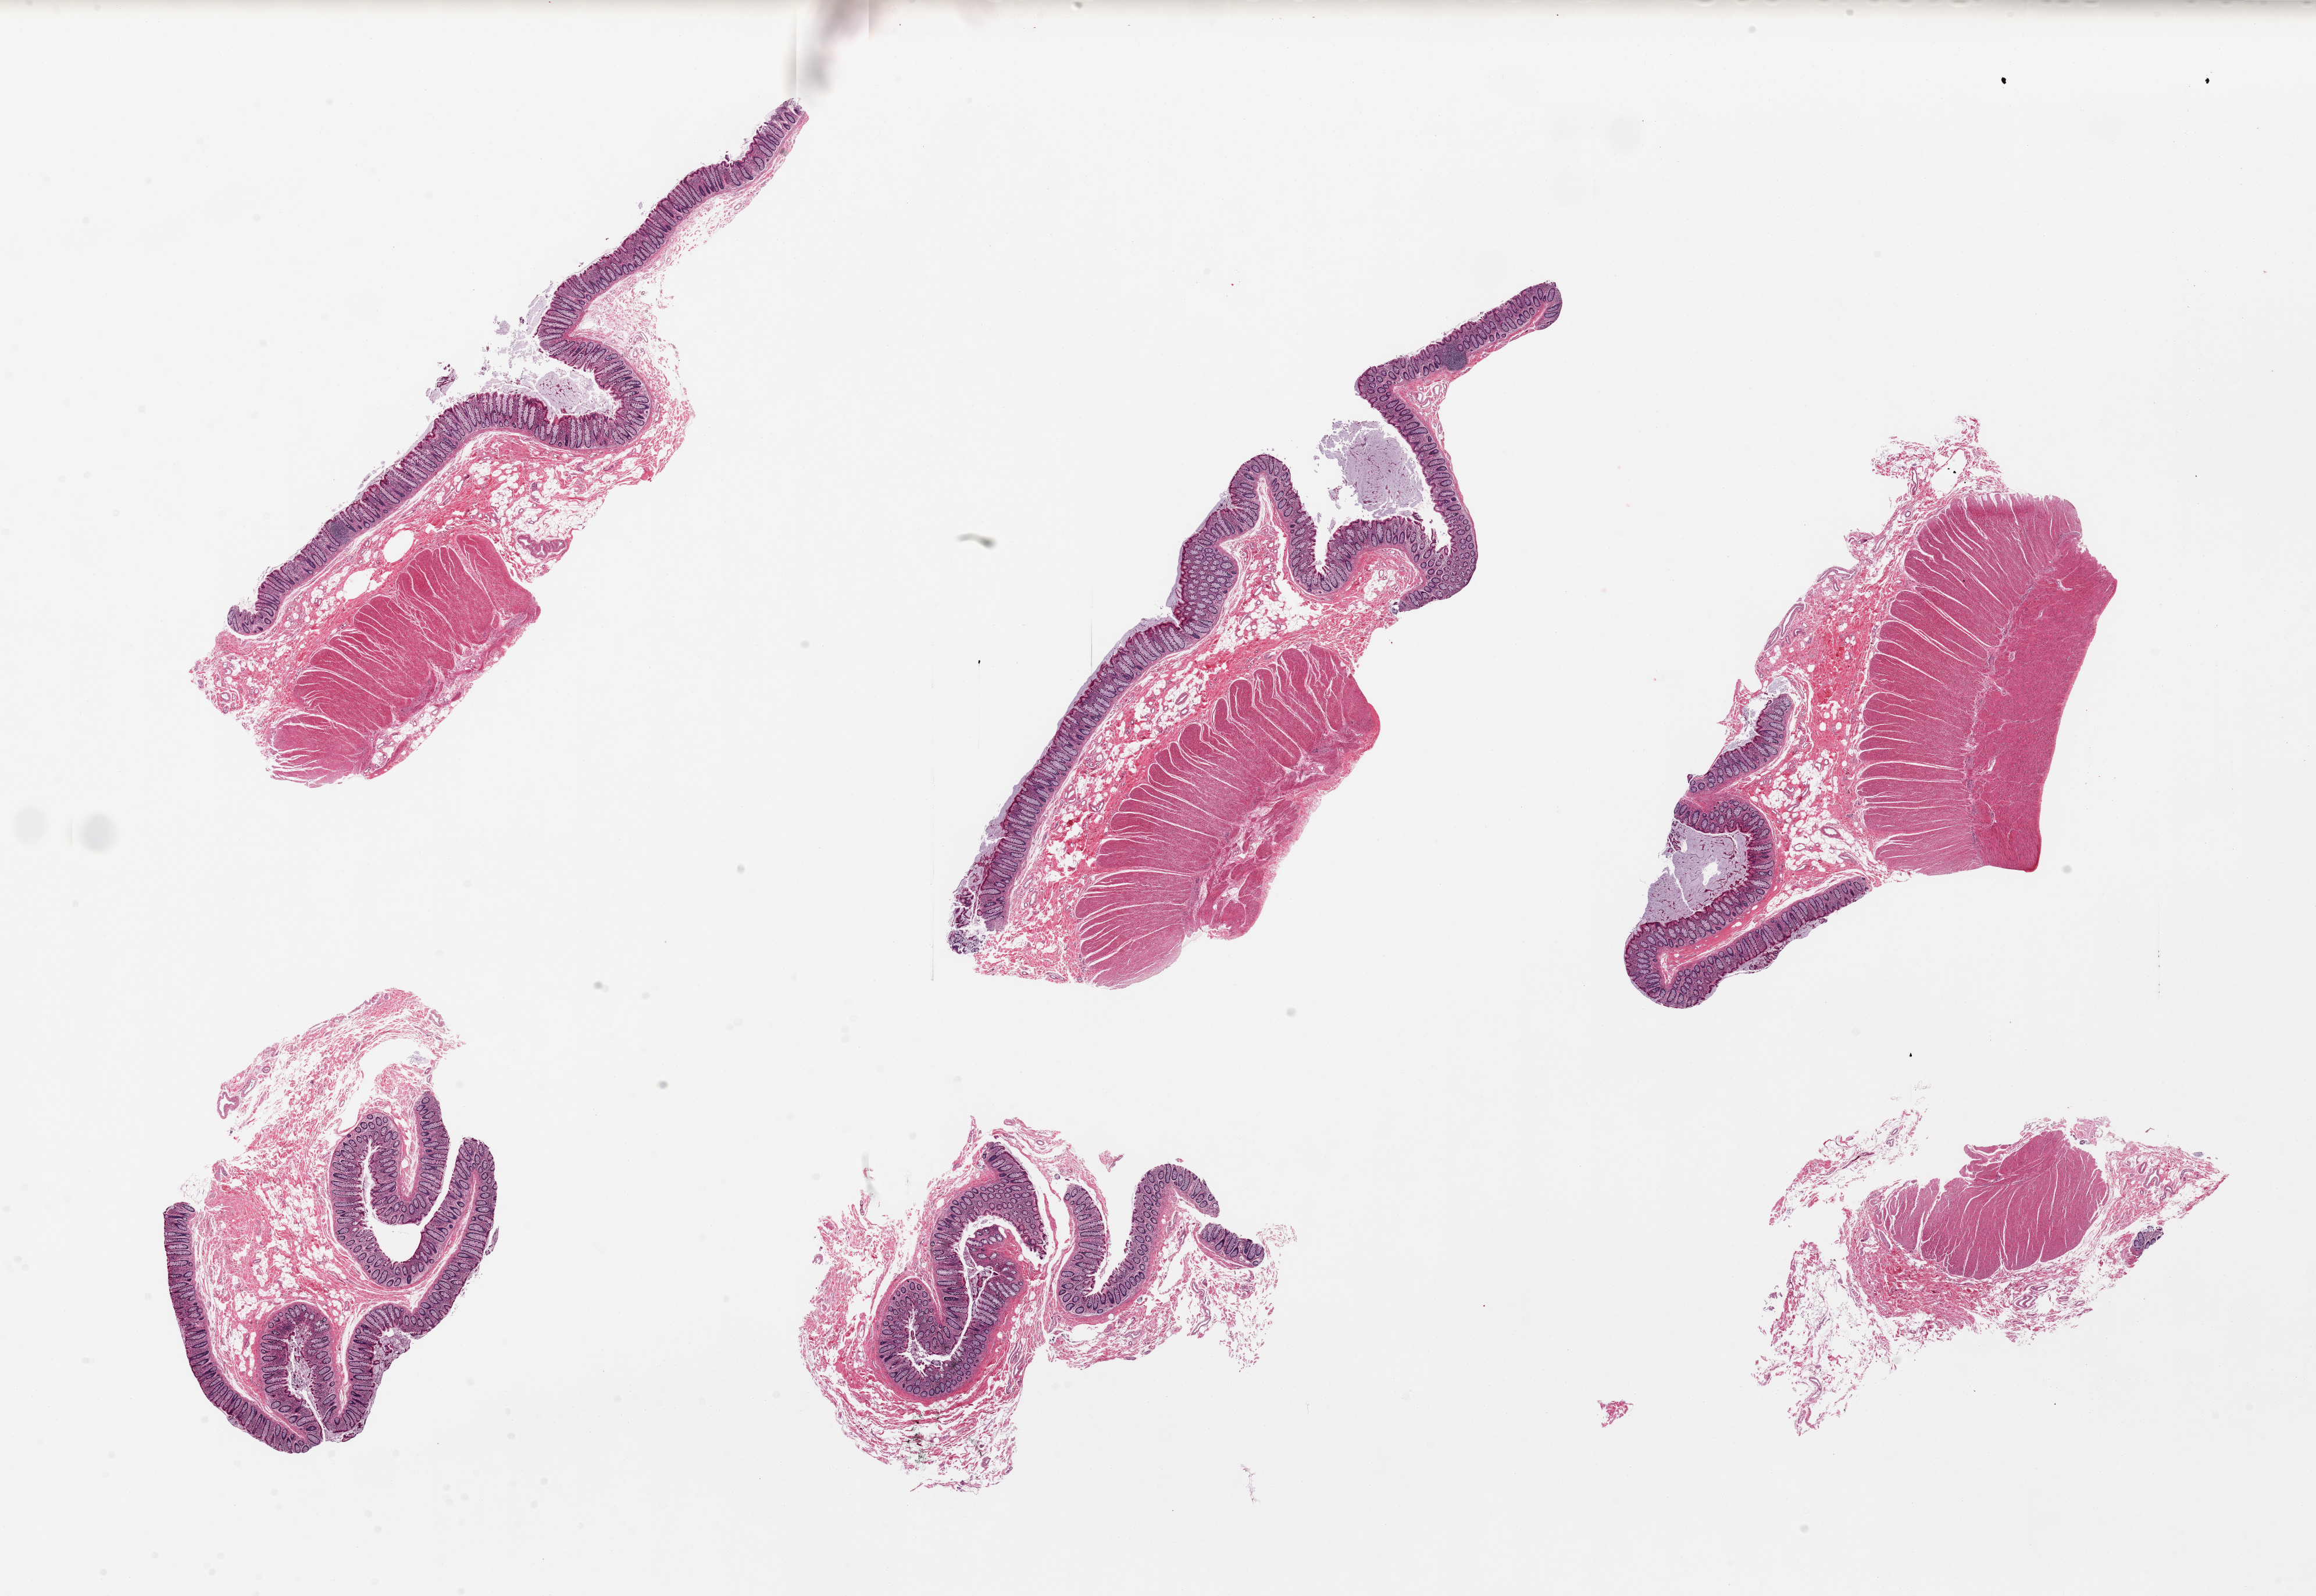
H&E whole-slide image — low-resolution overview of the scanned area, about 31.5 x 21.7 mm (from a 20x scan); PAXgene-fixed, paraffin-embedded tissue; section of sigmoid colon (target tissue); tissue donor sample.
Pathologist's review note for this sample: 6 pieces, 5 of 6 contain mucosa (not target), muscularis (target) present in 4.